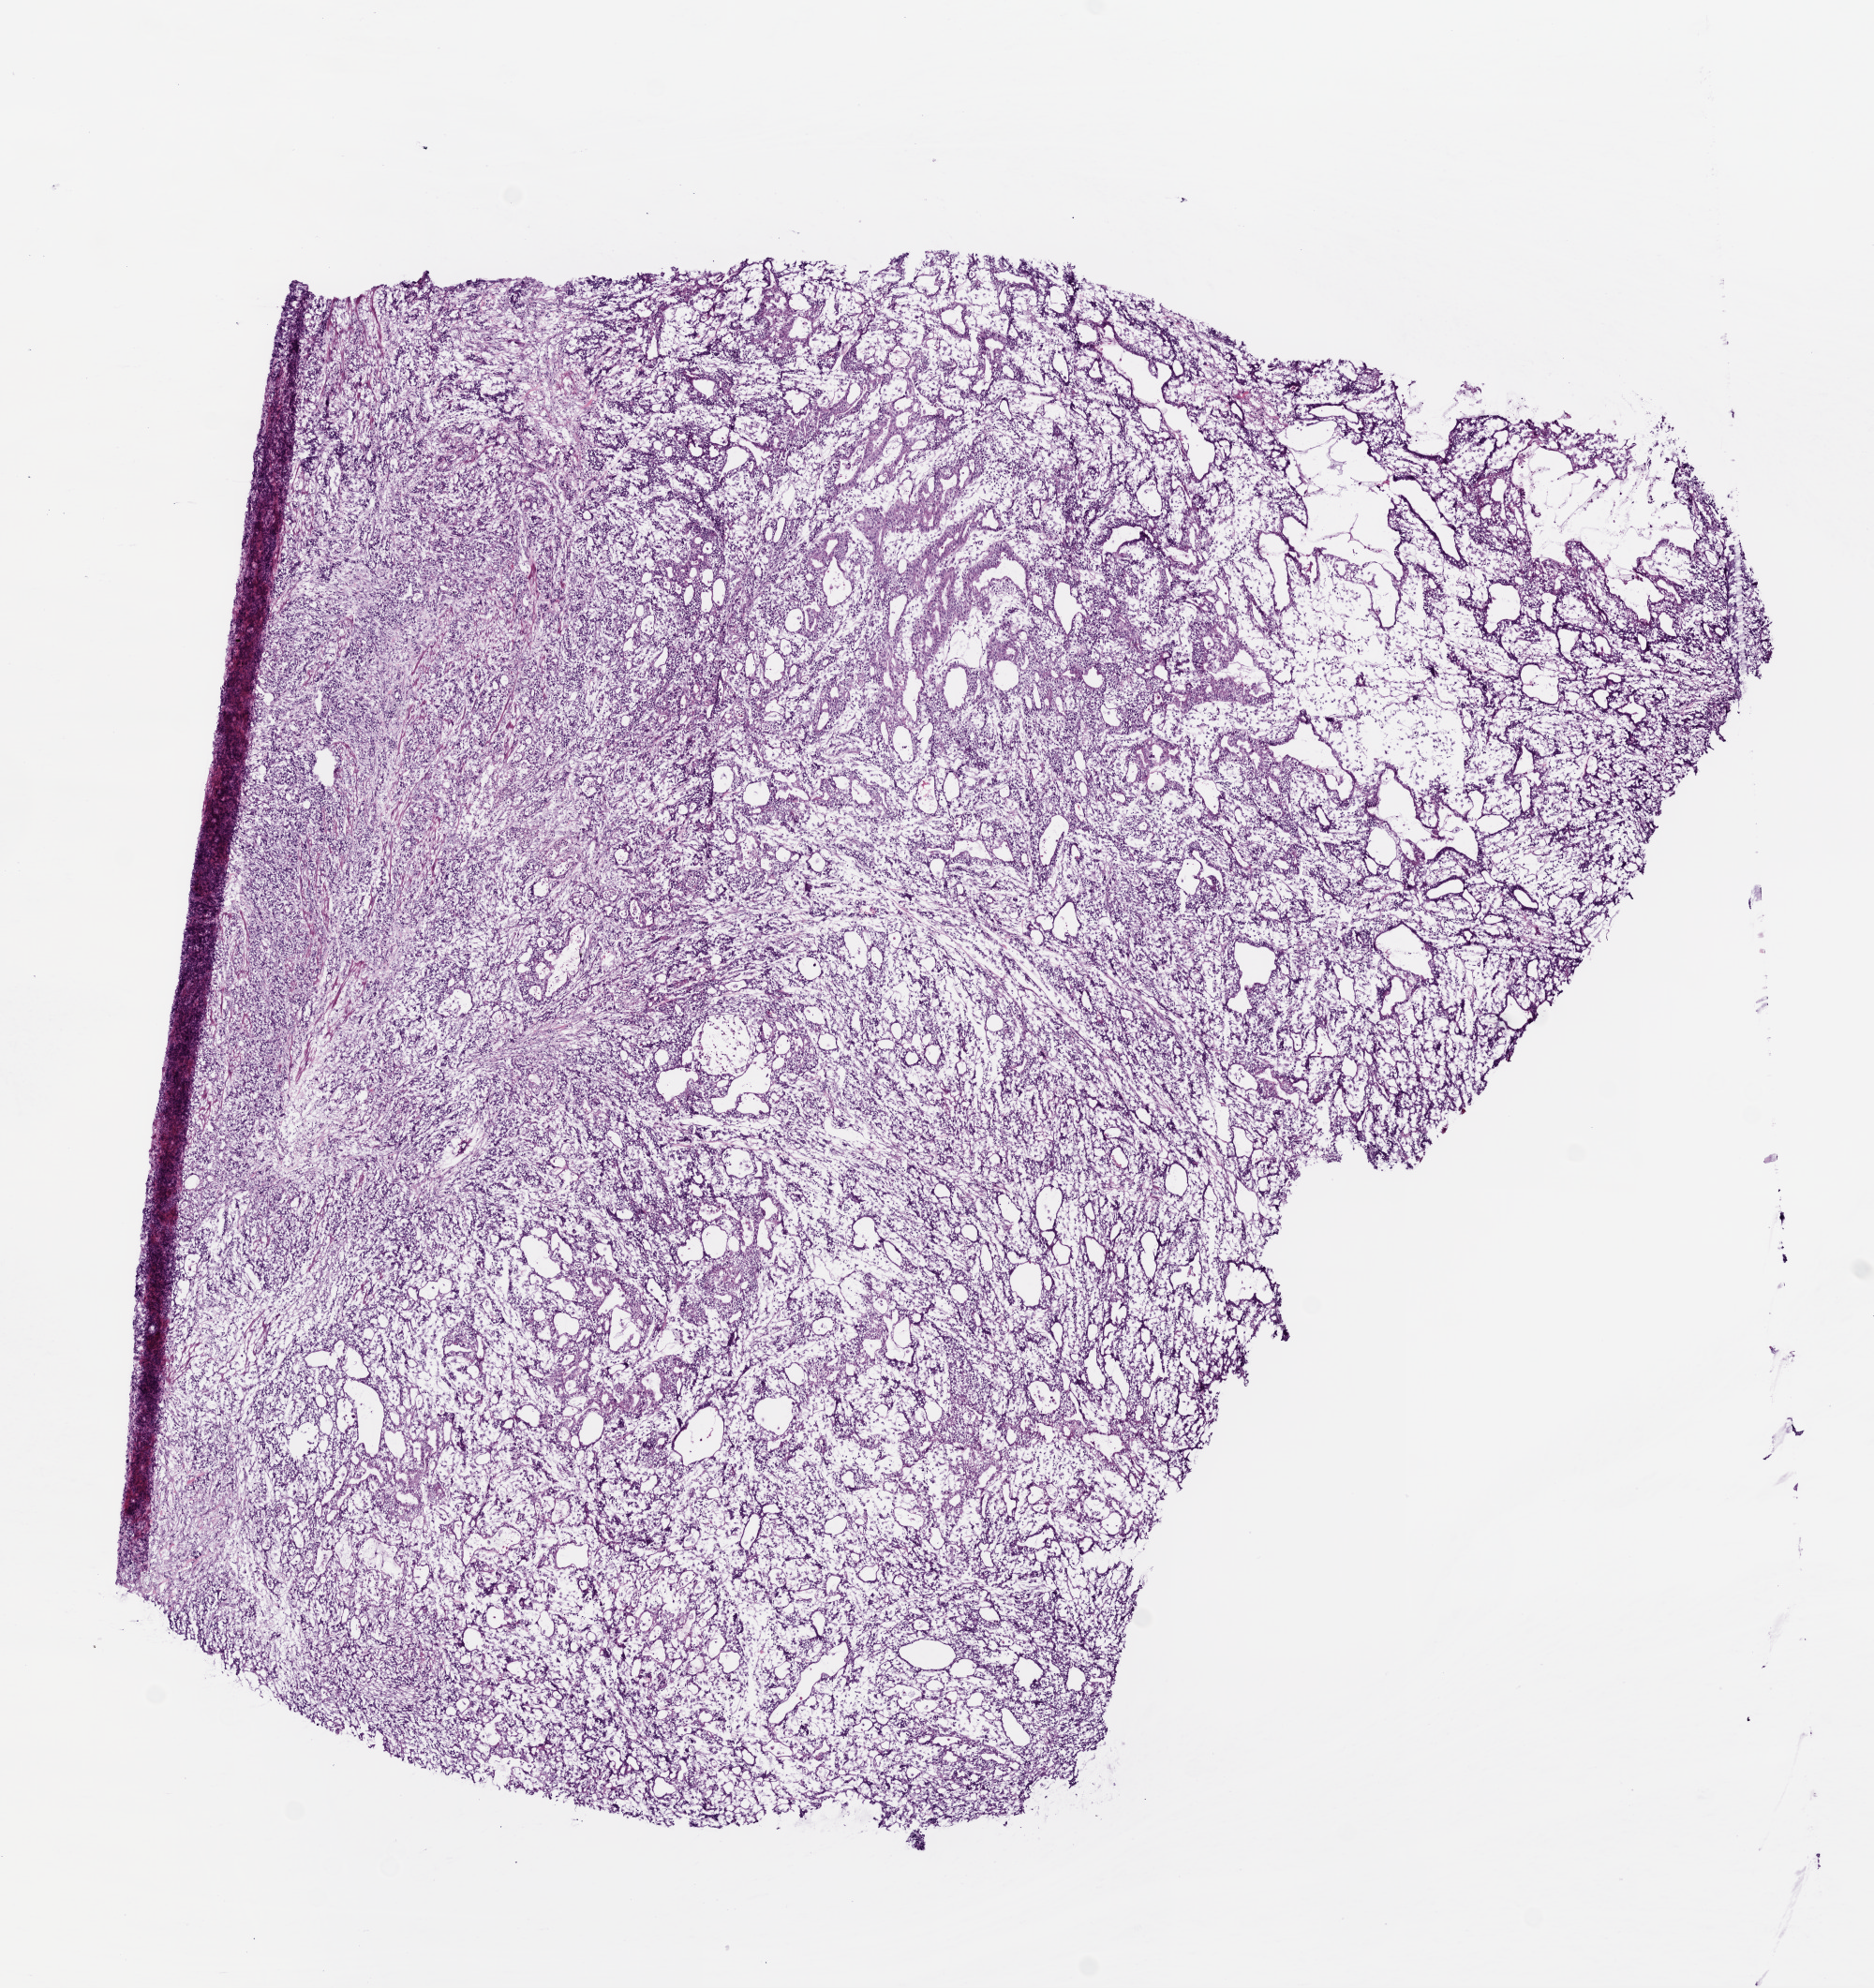
Digitized H&E-stained tissue section (whole slide) — low-resolution overview of the scanned area, about 8.0 x 8.5 mm. Frozen section. Primary tumour sample from the stomach. Patient: female, age at initial diagnosis 53 years. Histologic grade: G2 (moderately differentiated). Pathologist review of this section (percent, as recorded): tumour cells 85%, tumour nuclei 75%, normal cells 0%, stromal cells 15%, necrosis 0%.
• AJCC pathologic stage: IIIA (7th edition)
• pathologic diagnosis: Tubular adenocarcinoma (cardia, NOS)